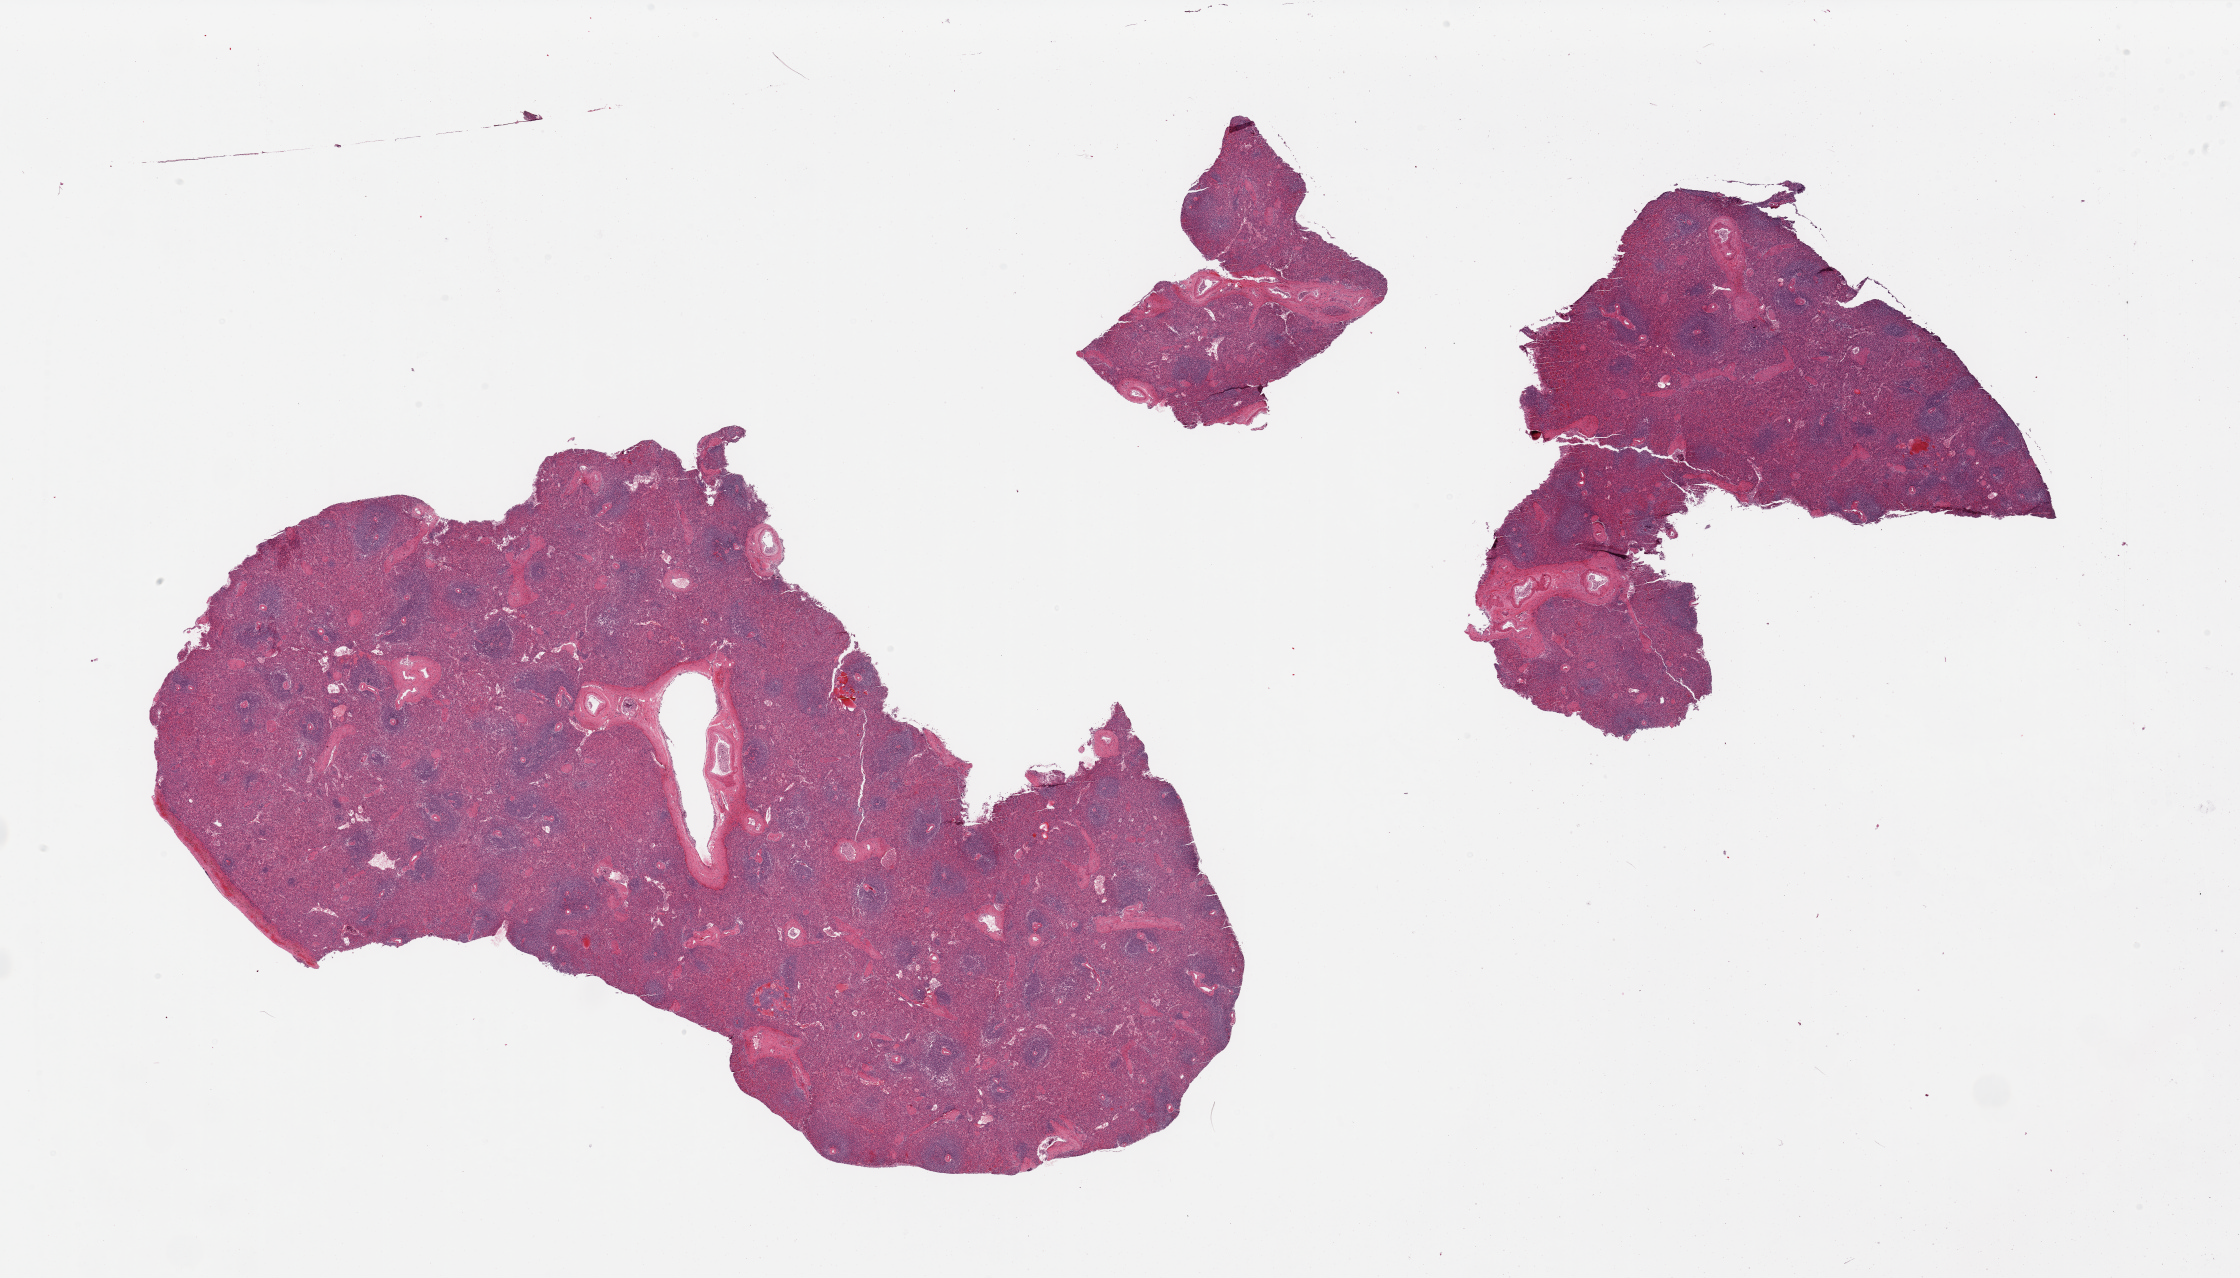
Whole-slide image, H&E stain — low-resolution overview of the scanned area, about 35.4 x 20.2 mm (acquisition: 20x scan), PAXgene-fixed, paraffin-embedded tissue, target tissue: spleen, donor tissue sample. Donor sex: female.
Reviewer comment on this tissue sample: 3 pieces, one piece includes capsule (preferred location is 5mm below capsule), some congestion.